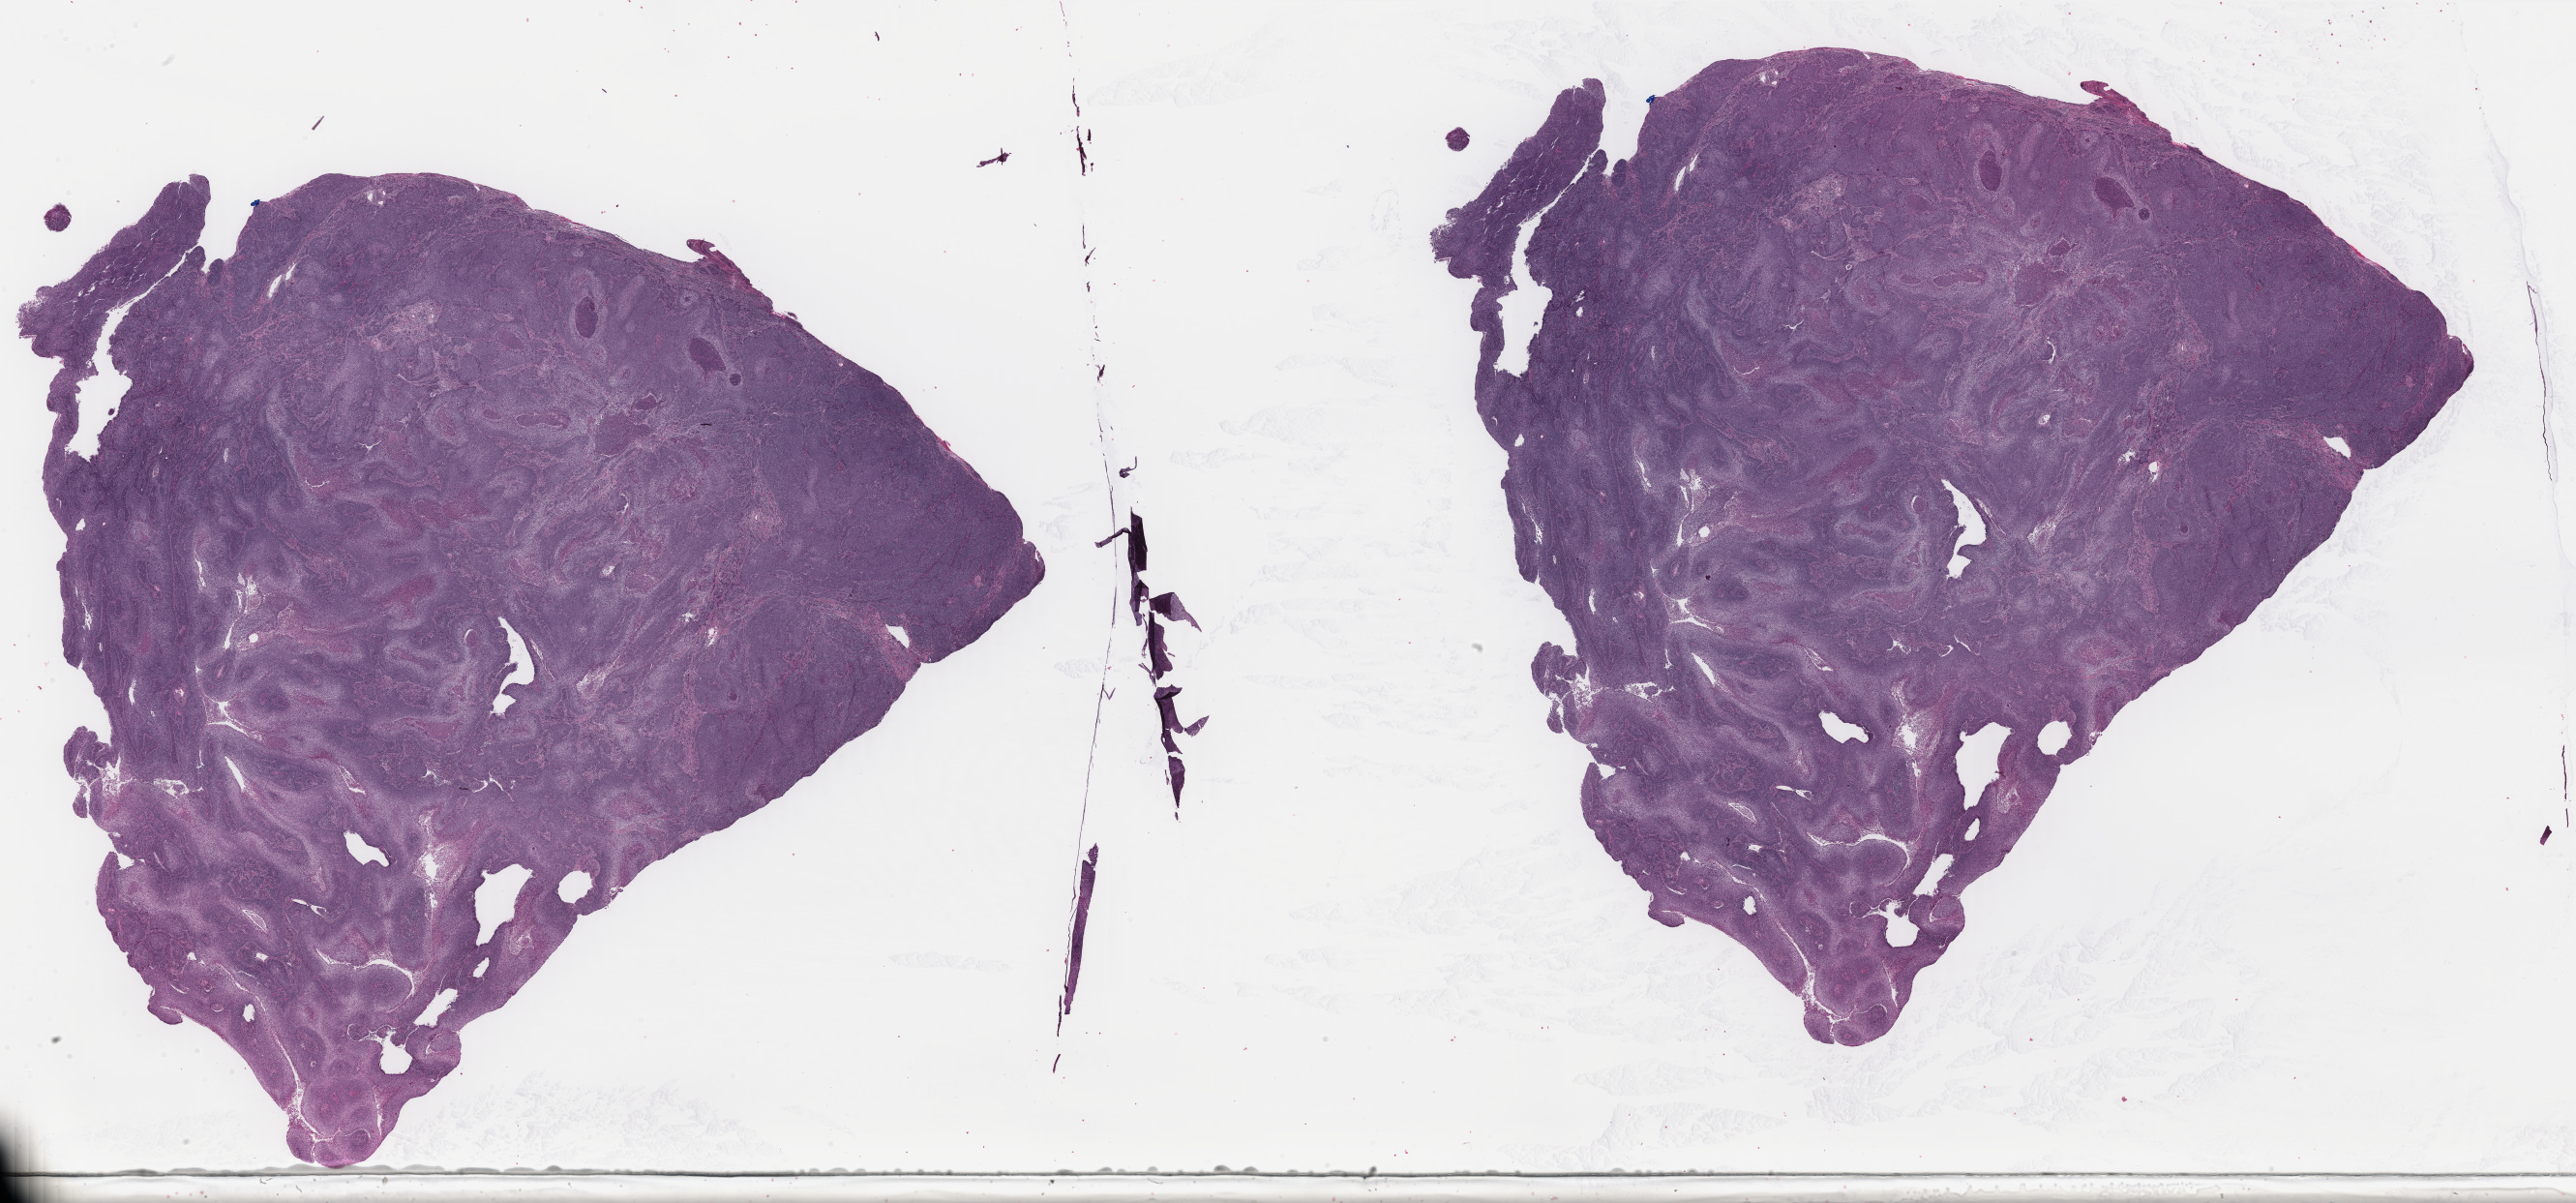
Whole-slide histology image, H&E — a low-resolution overview of the entire scanned area, about 42.1 x 19.7 mm (slide scanned at 40x); formalin-fixed paraffin-embedded (FFPE) diagnostic section; primary tumour sample from the cervix. Female, age 62 years at initial diagnosis.
Pathologic diagnosis: Squamous cell carcinoma, large cell, nonkeratinizing, NOS (cervix uteri).